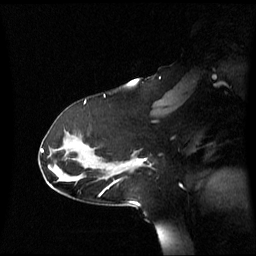
Breast MRI (dynamic contrast-enhanced), one sagittal slice. Slice 39 of 60 in the series (ordered by position). Dynamic contrast-enhanced series, image 2 of 3 at this slice position (ordered by acquisition). 1.5 T. TE 4.2 ms, TR 8.4 ms. 256 × 256 image matrix, field of view 270 × 270 mm. Patient: female, 39 years. From the clinical record (not read from this slice): setting: breast cancer imaged before/during neoadjuvant chemotherapy; receptor status: triple-negative.
Outlined on this slice (semi-automatic segmentation, software-assisted and operator-edited):
- analysis volume of interest (the breast-tissue region the enhancement analysis was run in; not a lesion): box from (x=117, y=152) to (x=151, y=174) px
- tumour enhancement mask (voxels above the 70 % enhancement threshold inside the analysis volume of interest): (x=135, y=158)–(x=146, y=164)